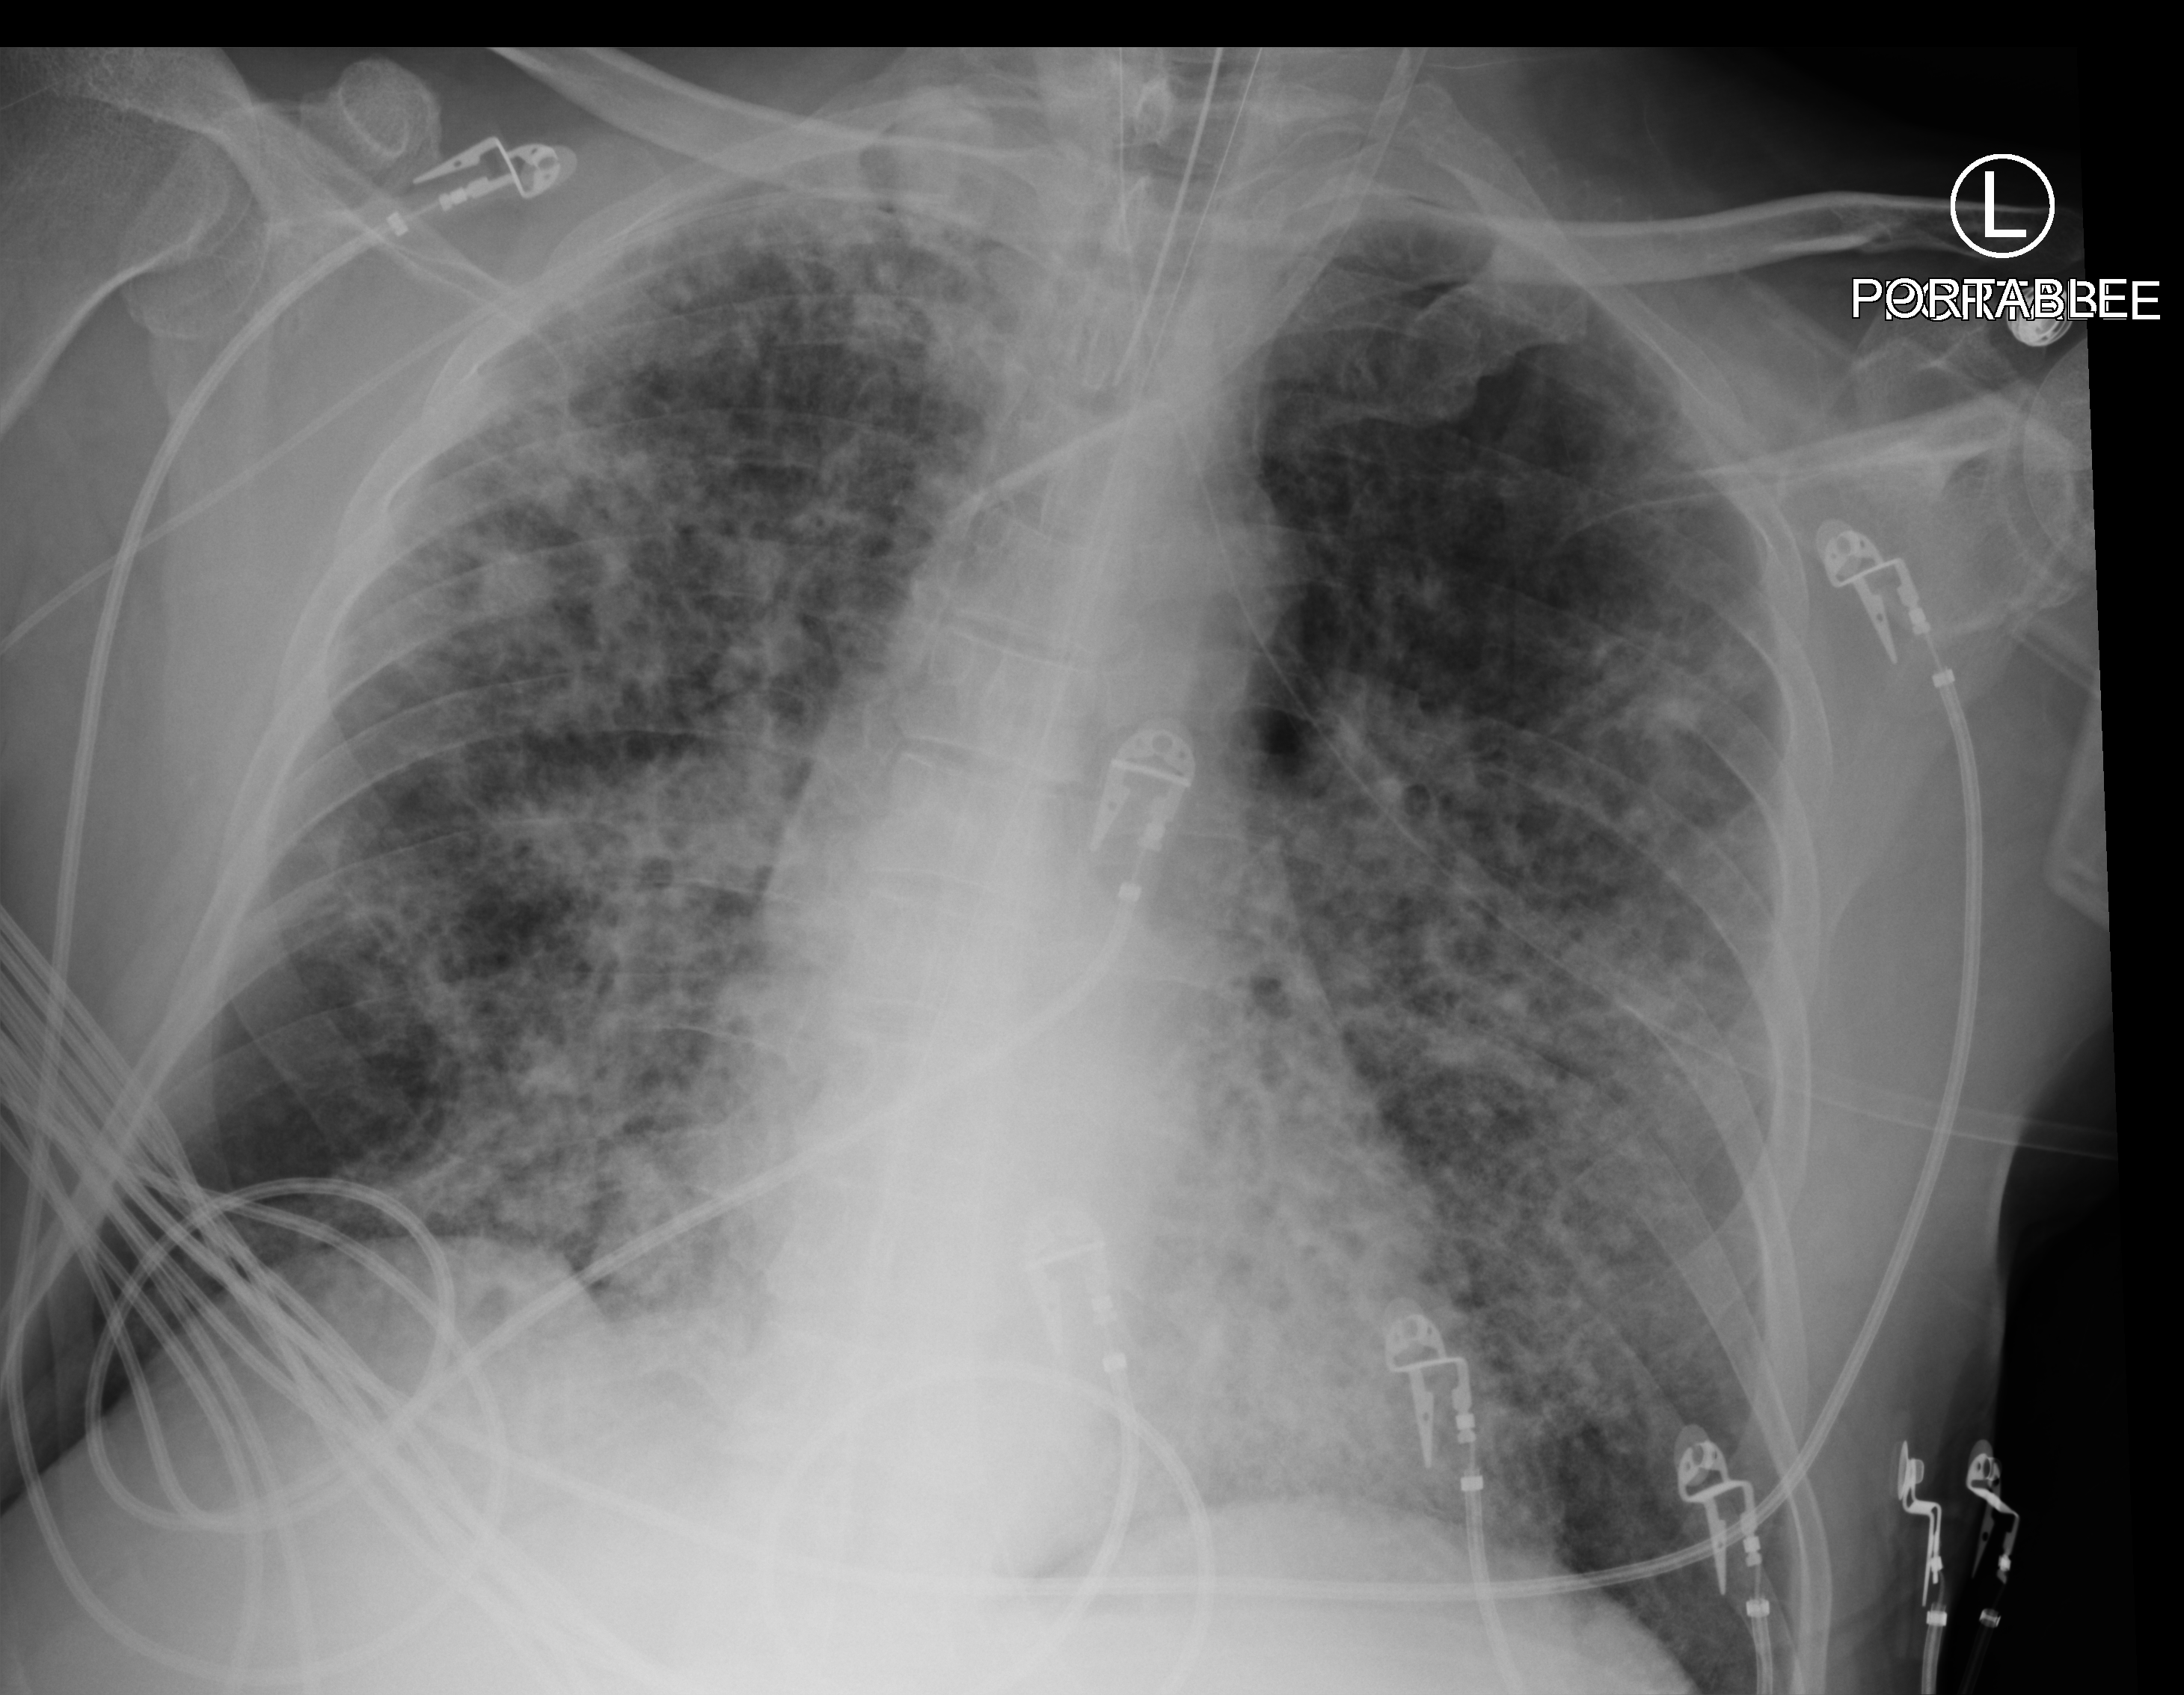
Chest X-ray (portable); anteroposterior (AP) projection. Patient hospitalised with COVID-19; male, aged 60–74 years.
Hospital-stay facts (about this admission, not read from this image; timing relative to this image not recorded): admitted to intensive care during this hospital stay: yes; mechanically ventilated during this hospital stay: yes.